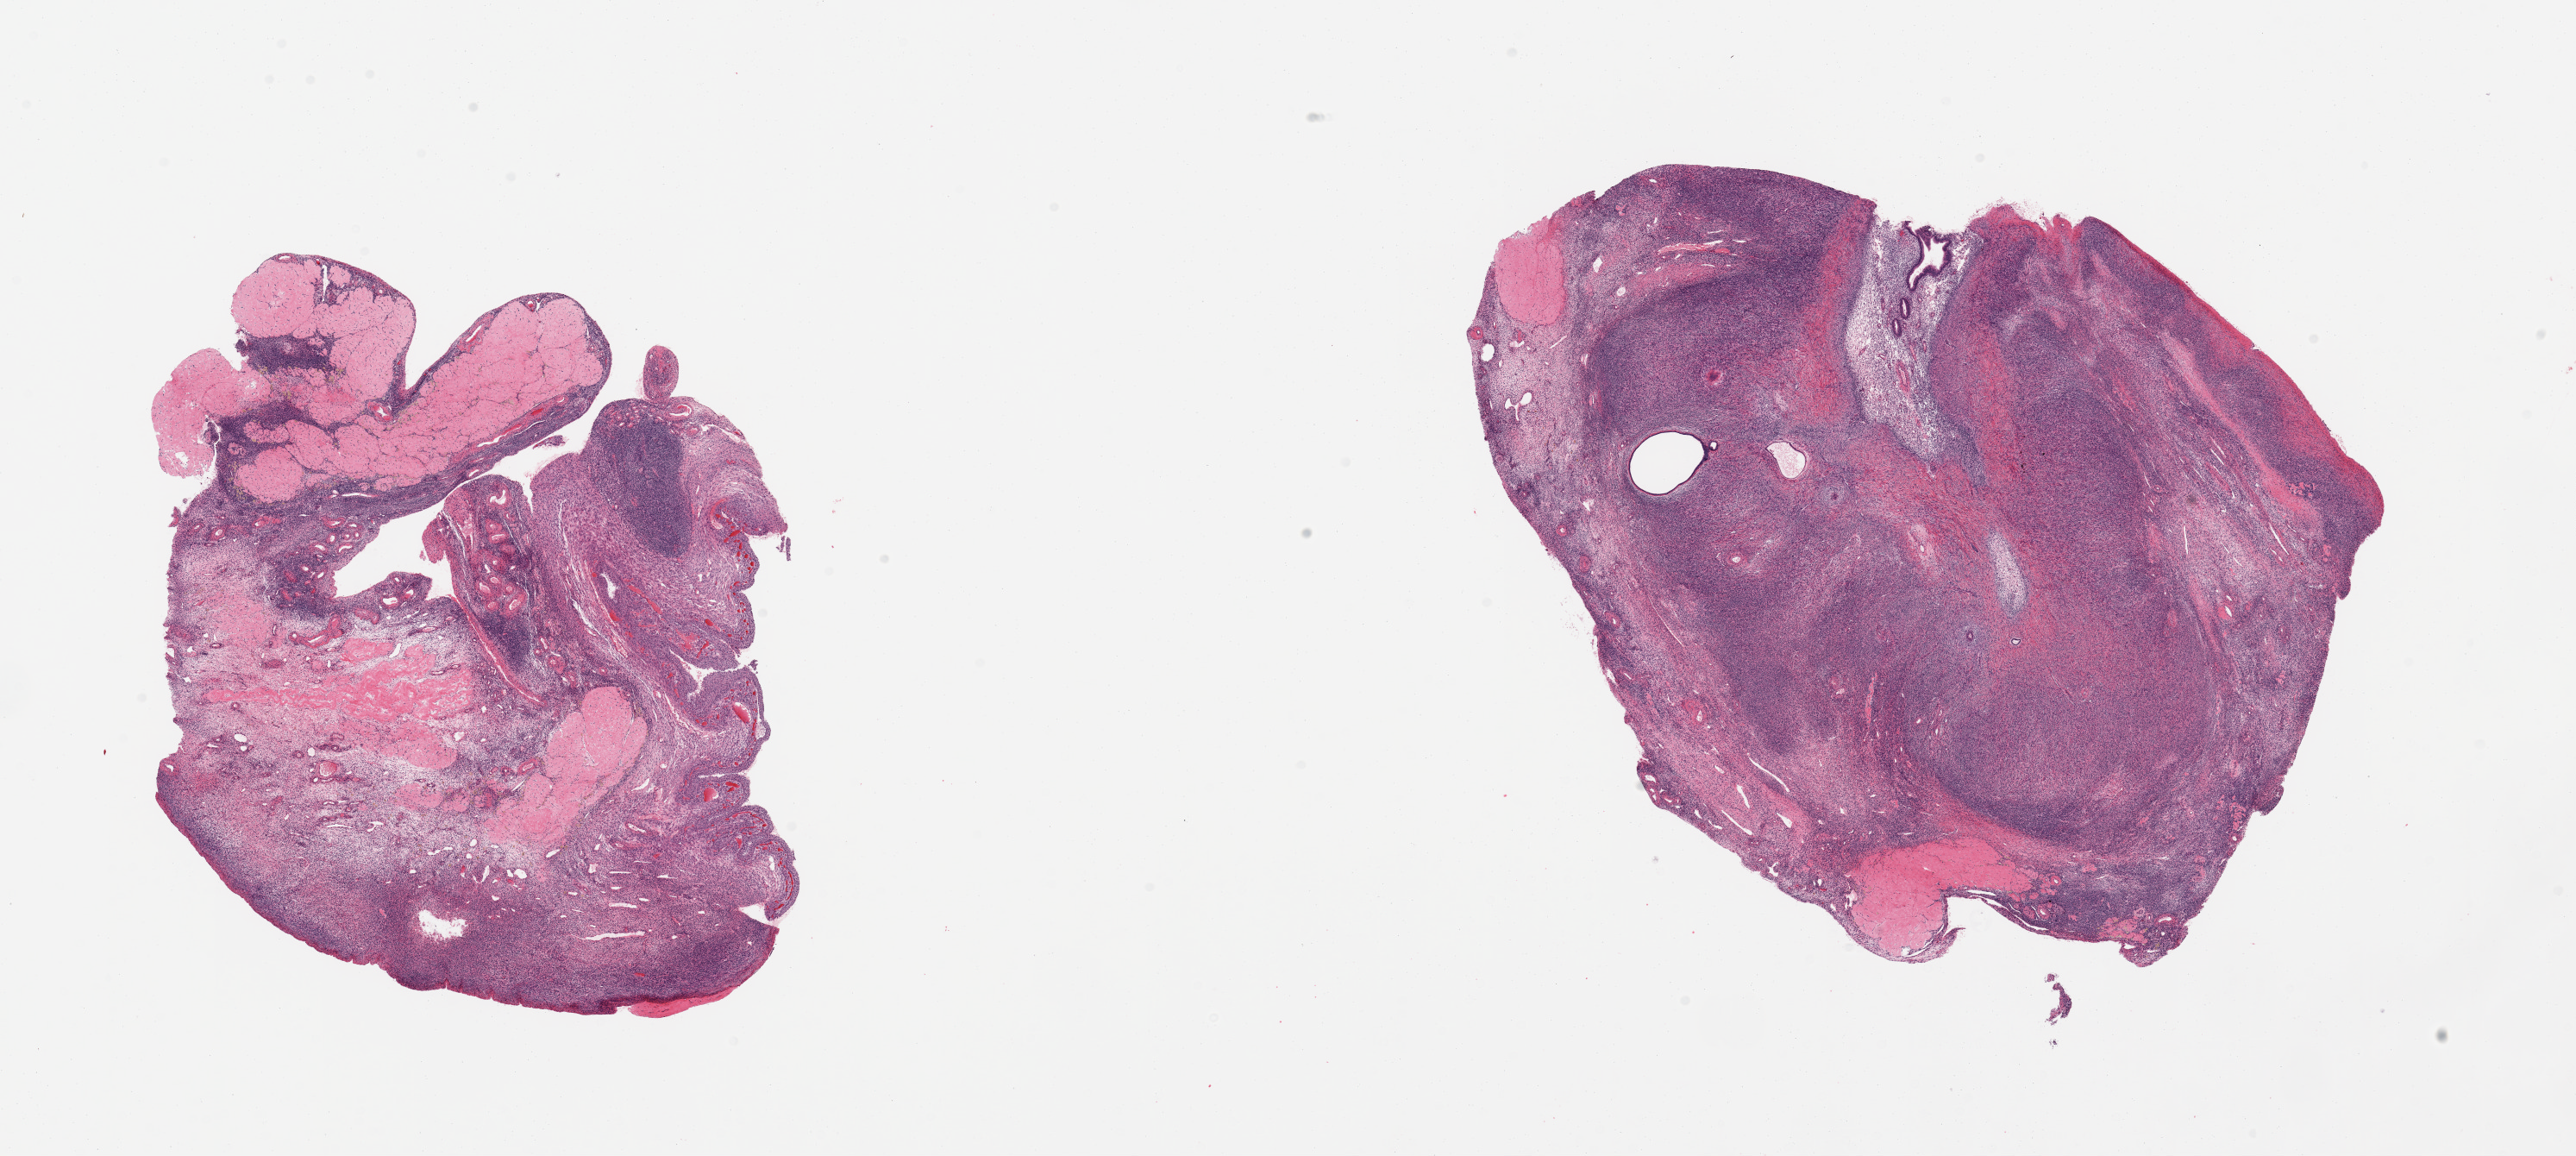
Whole-slide image, hematoxylin and eosin (H&E) stain, low-resolution overview of the scanned area, about 23.6 x 10.6 mm (acquisition: 20x scan), PAXgene-fixed, paraffin-embedded tissue, section of ovary (target tissue), tissue donor sample.
Review note (as recorded): 2 pieces; focus of endometriosis.